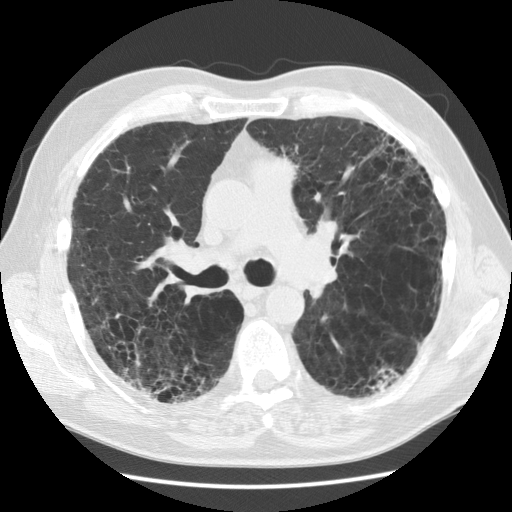
Low-dose screening chest CT, one axial slice. Slice 75 of 128 in the series (ordered by position). Reconstruction kernel STANDARD. 120 kVp. Lung window (W 1500 / L -600 HU). 2.5 mm slice thickness. 512 × 512 image matrix.
Annotated regions visible in this slice (outlined manually by an expert reader):
- lesion 1 (tumor, lower lobe of left lung): bounding box <368,367,401,393> (left, top, right, bottom; pixels)